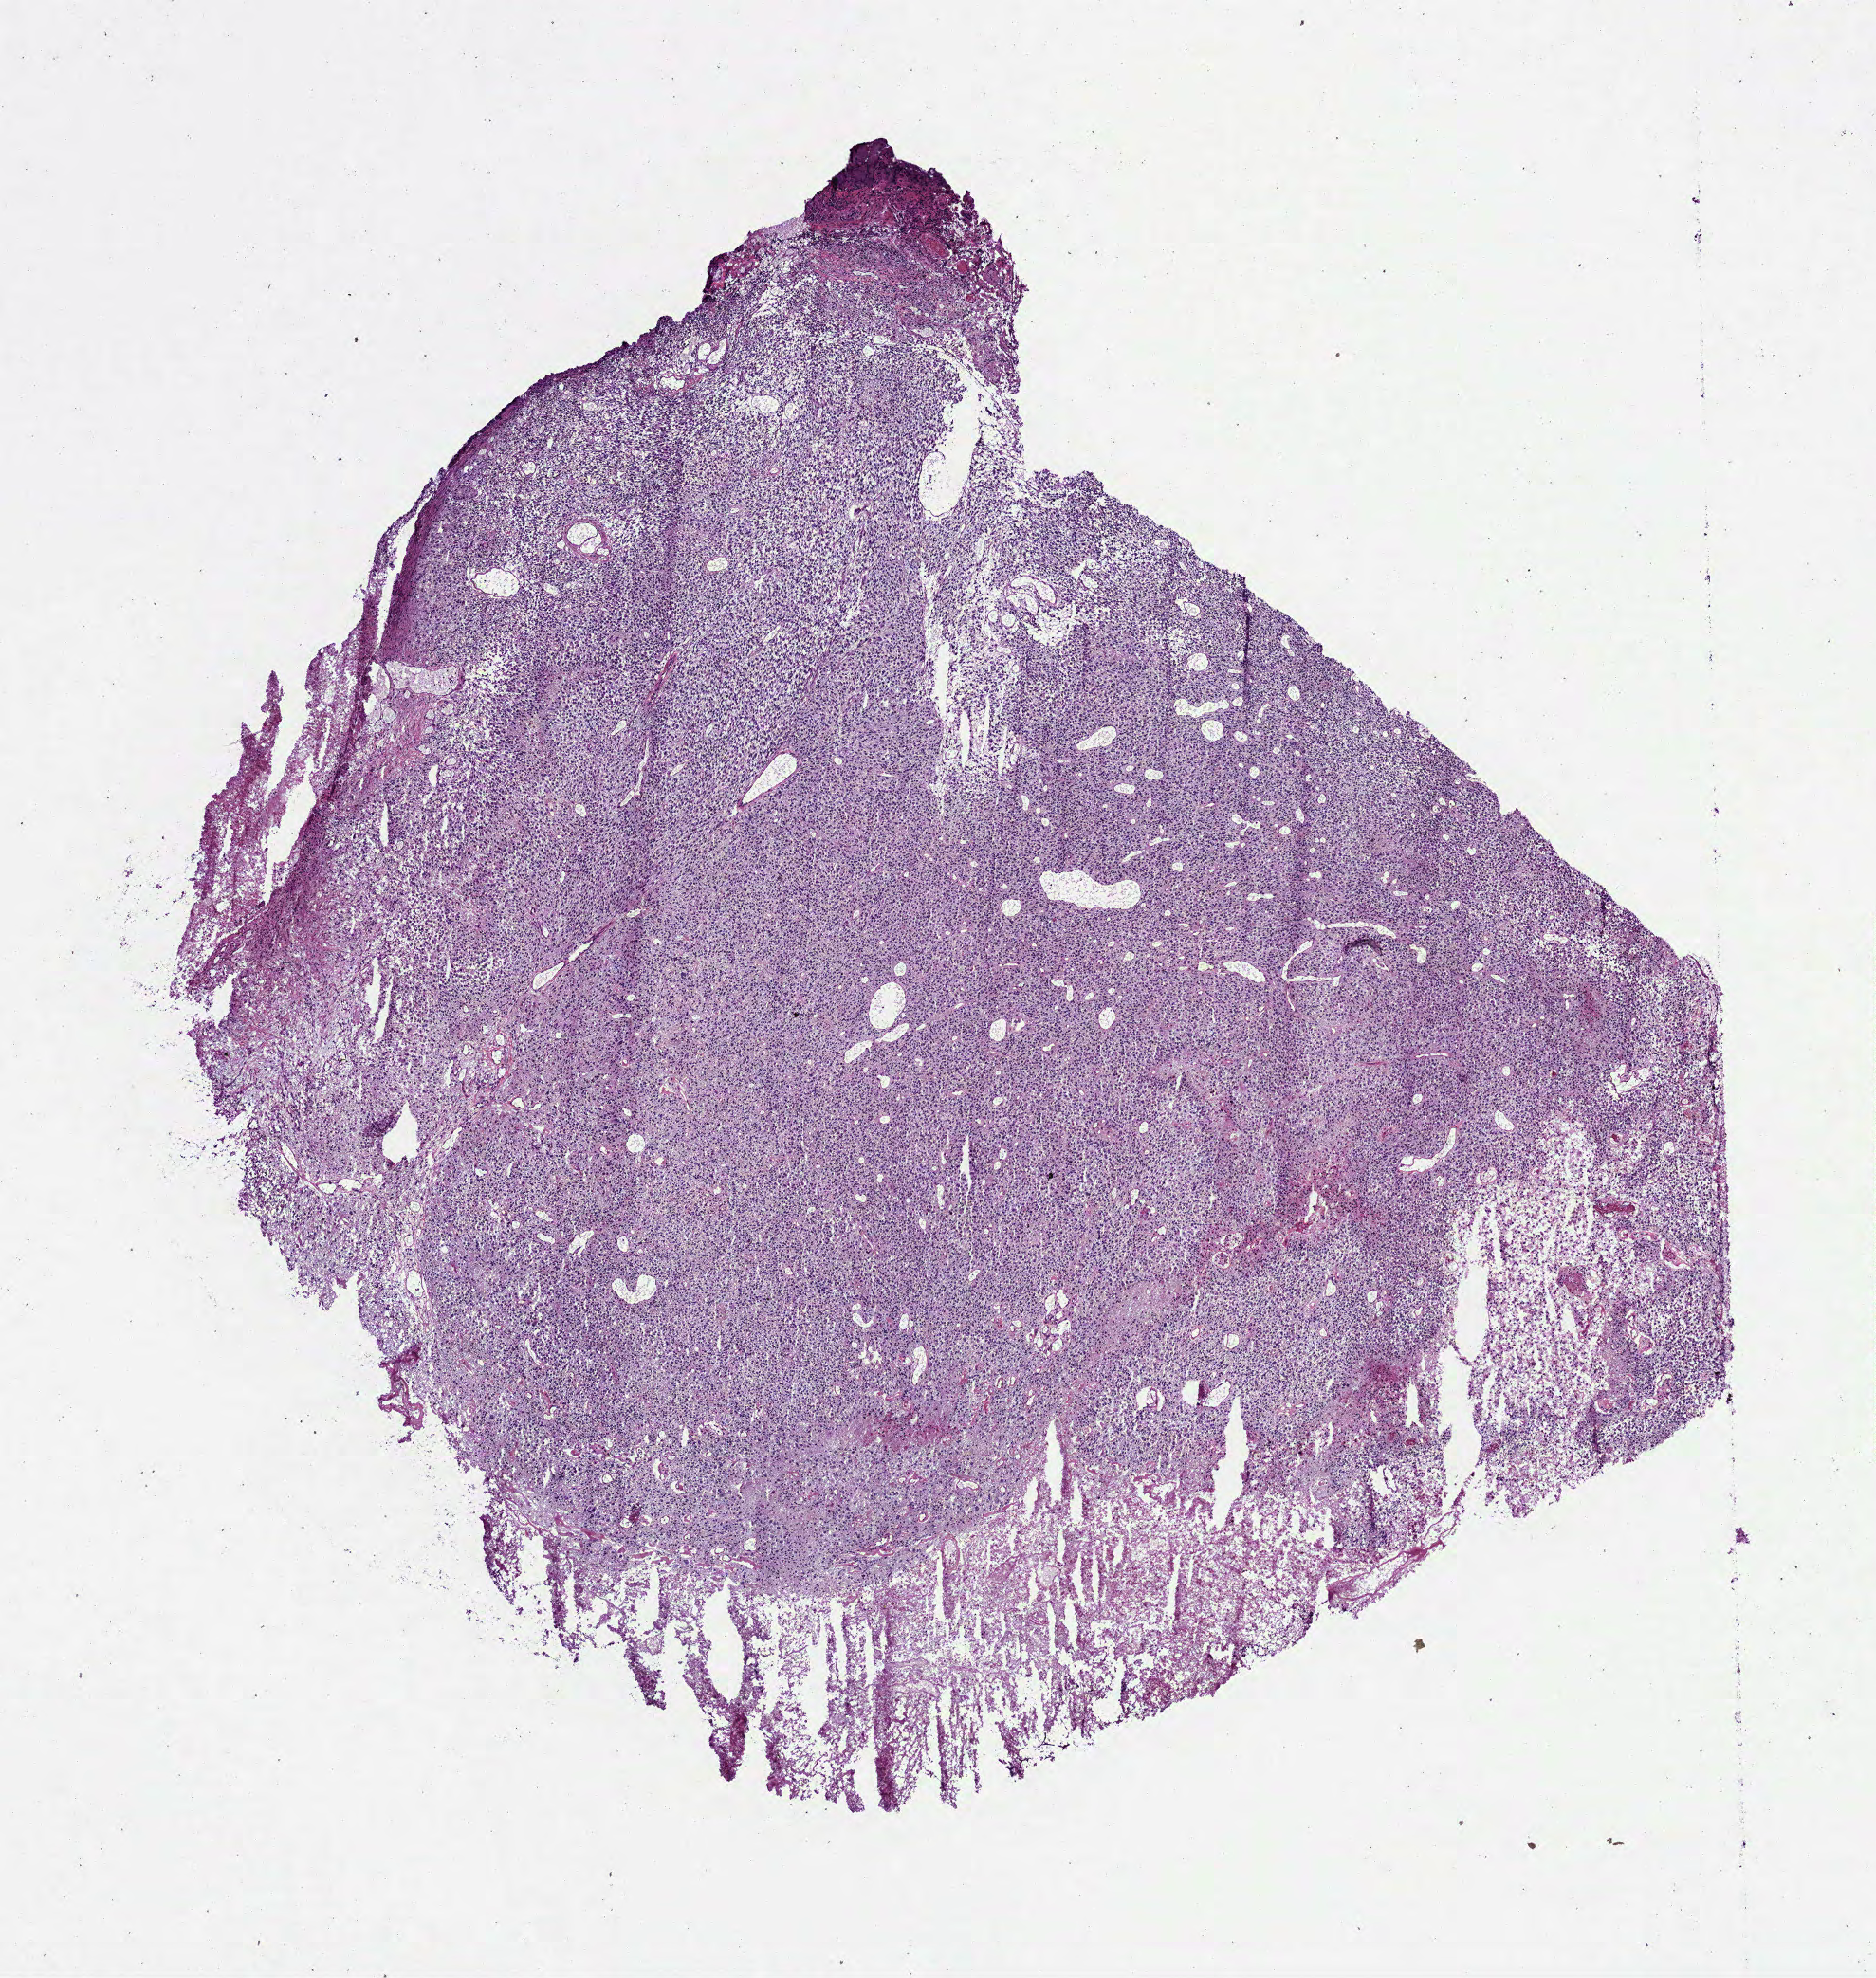
H&E-stained whole-slide image — a low-resolution overview of the entire scanned area, about 8.0 x 8.4 mm, frozen section, primary tumour sample from the brain. Male, age 64 years at initial diagnosis. Pathologist review of this section (percent, as recorded): tumour cells 85%, tumour nuclei 80%, normal cells 0%, stromal cells 0%, necrosis 15%.
Pathologic diagnosis: Glioblastoma.